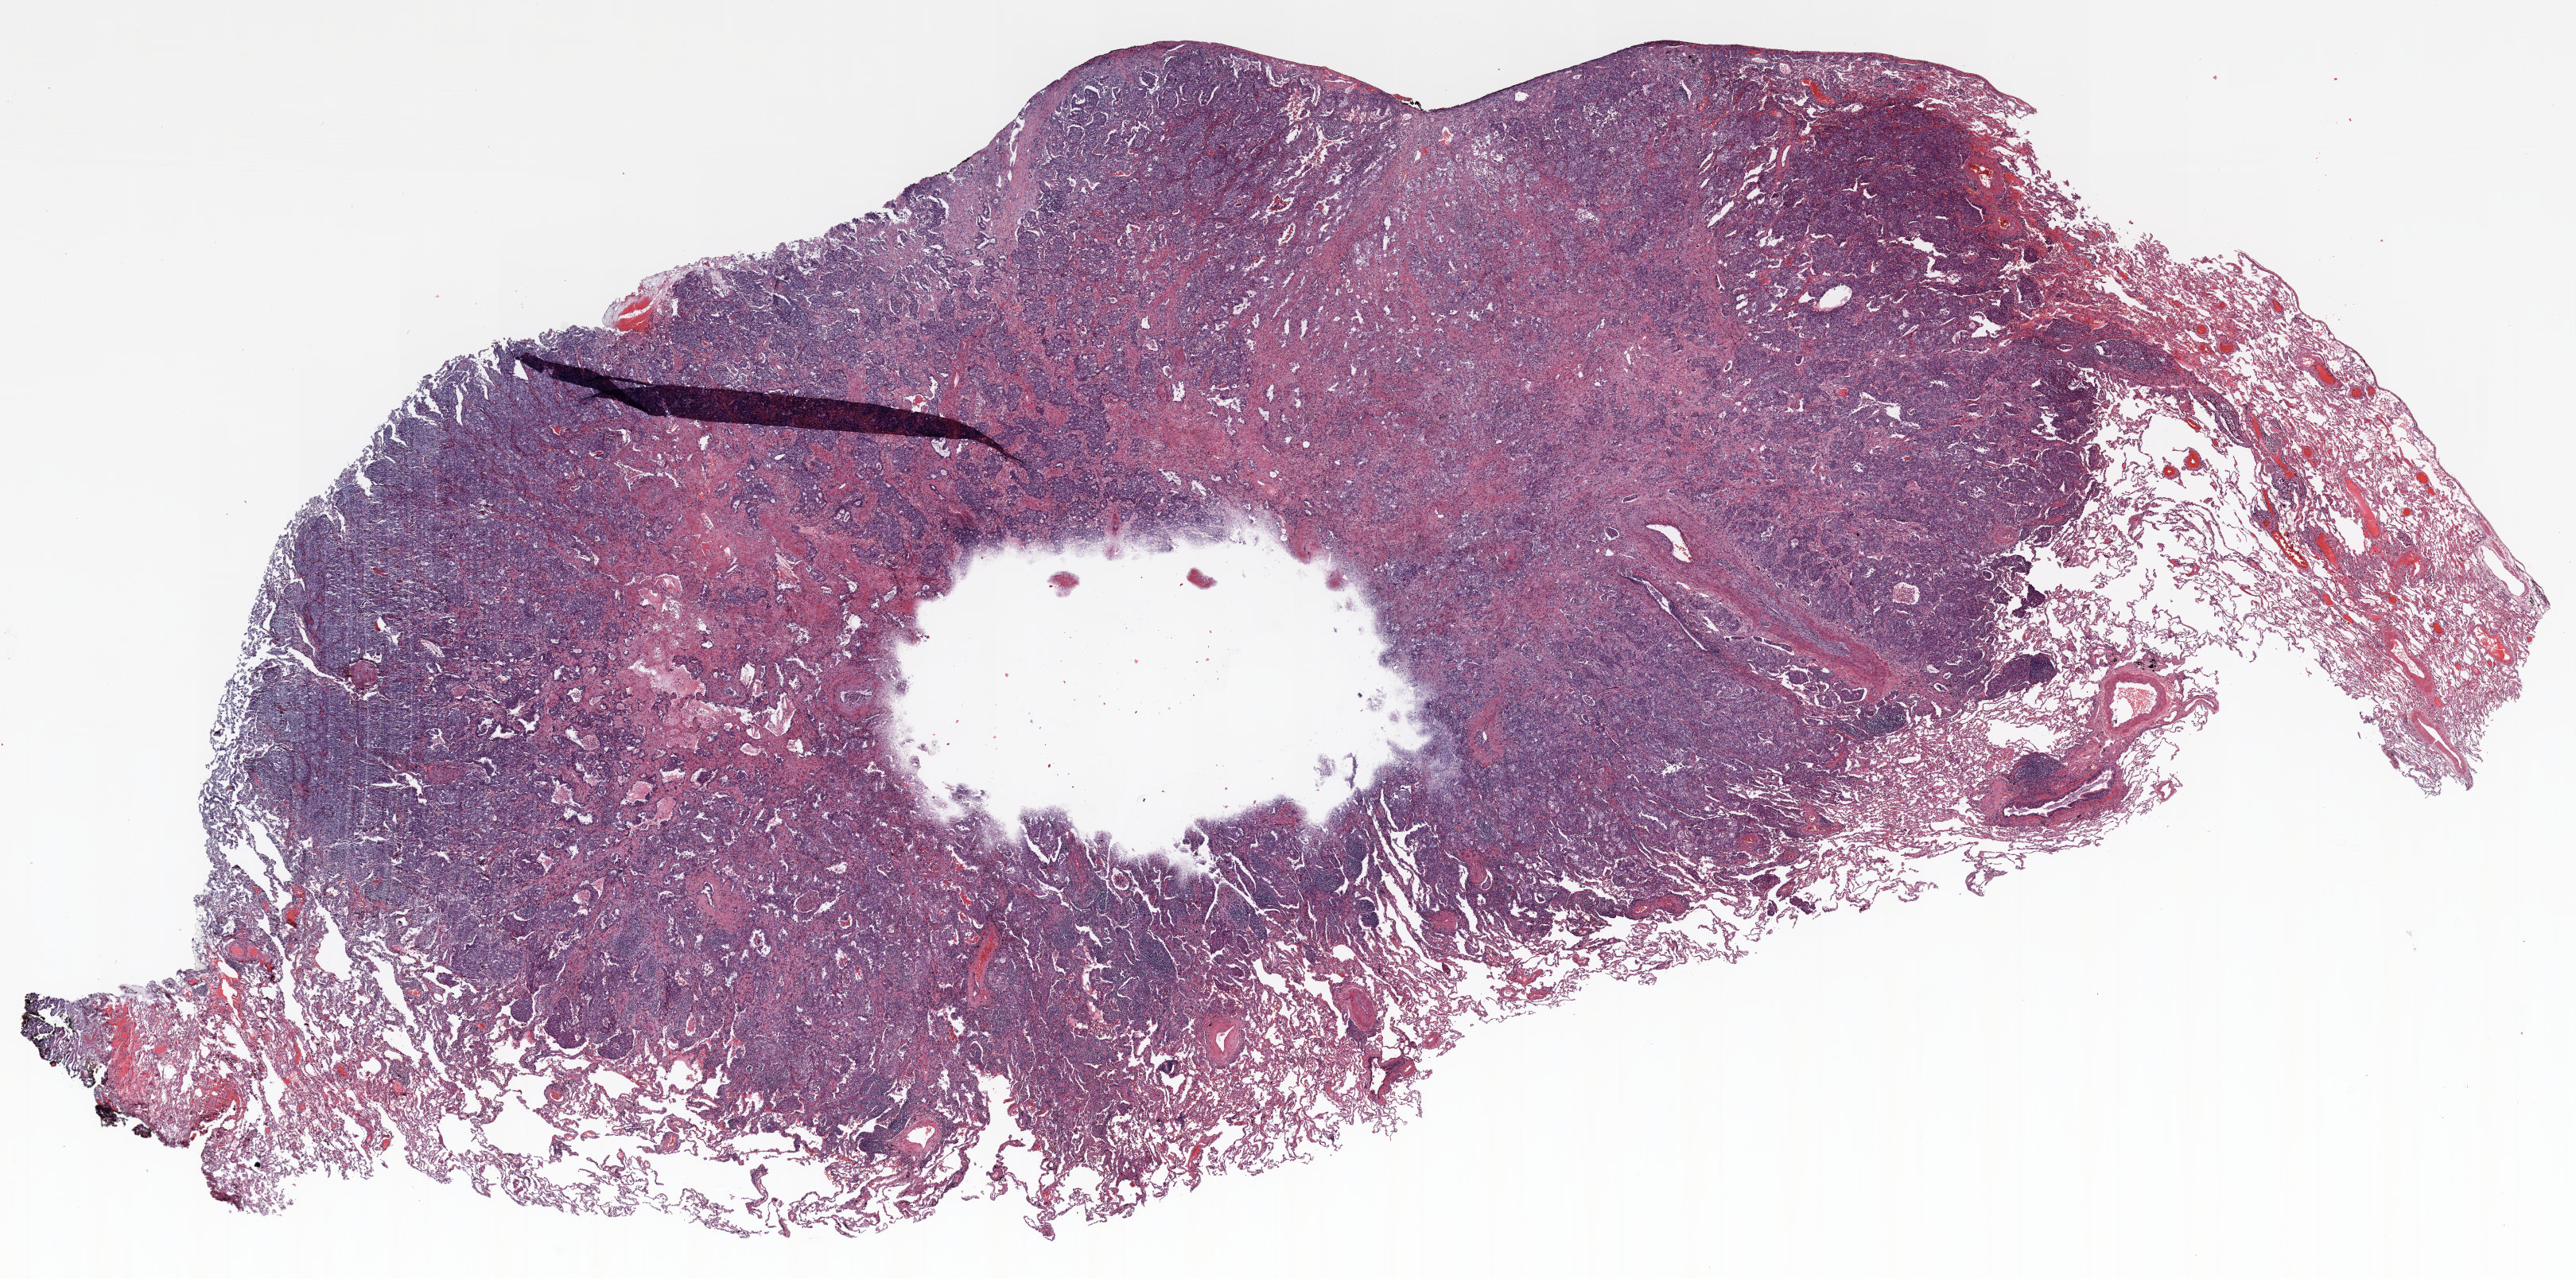
Whole-slide histology image, Hematoxylin and eosin (H&E) stained — low-resolution overview of the scanned area, about 26.0 x 12.9 mm; FFPE section; lung. Female, age 59 at enrolment. Former smoker at enrolment. Grade: moderately differentiated (G2).
ICD-O-3 topography: lower lobe of lung (C34.3). Stage (AJCC 6th edition): IIB. Tumour size (pathology): 22 mm. Participant's lung-cancer diagnosis: Adenocarcinoma, NOS. Primary tumour location (clinical record): right lower lobe.